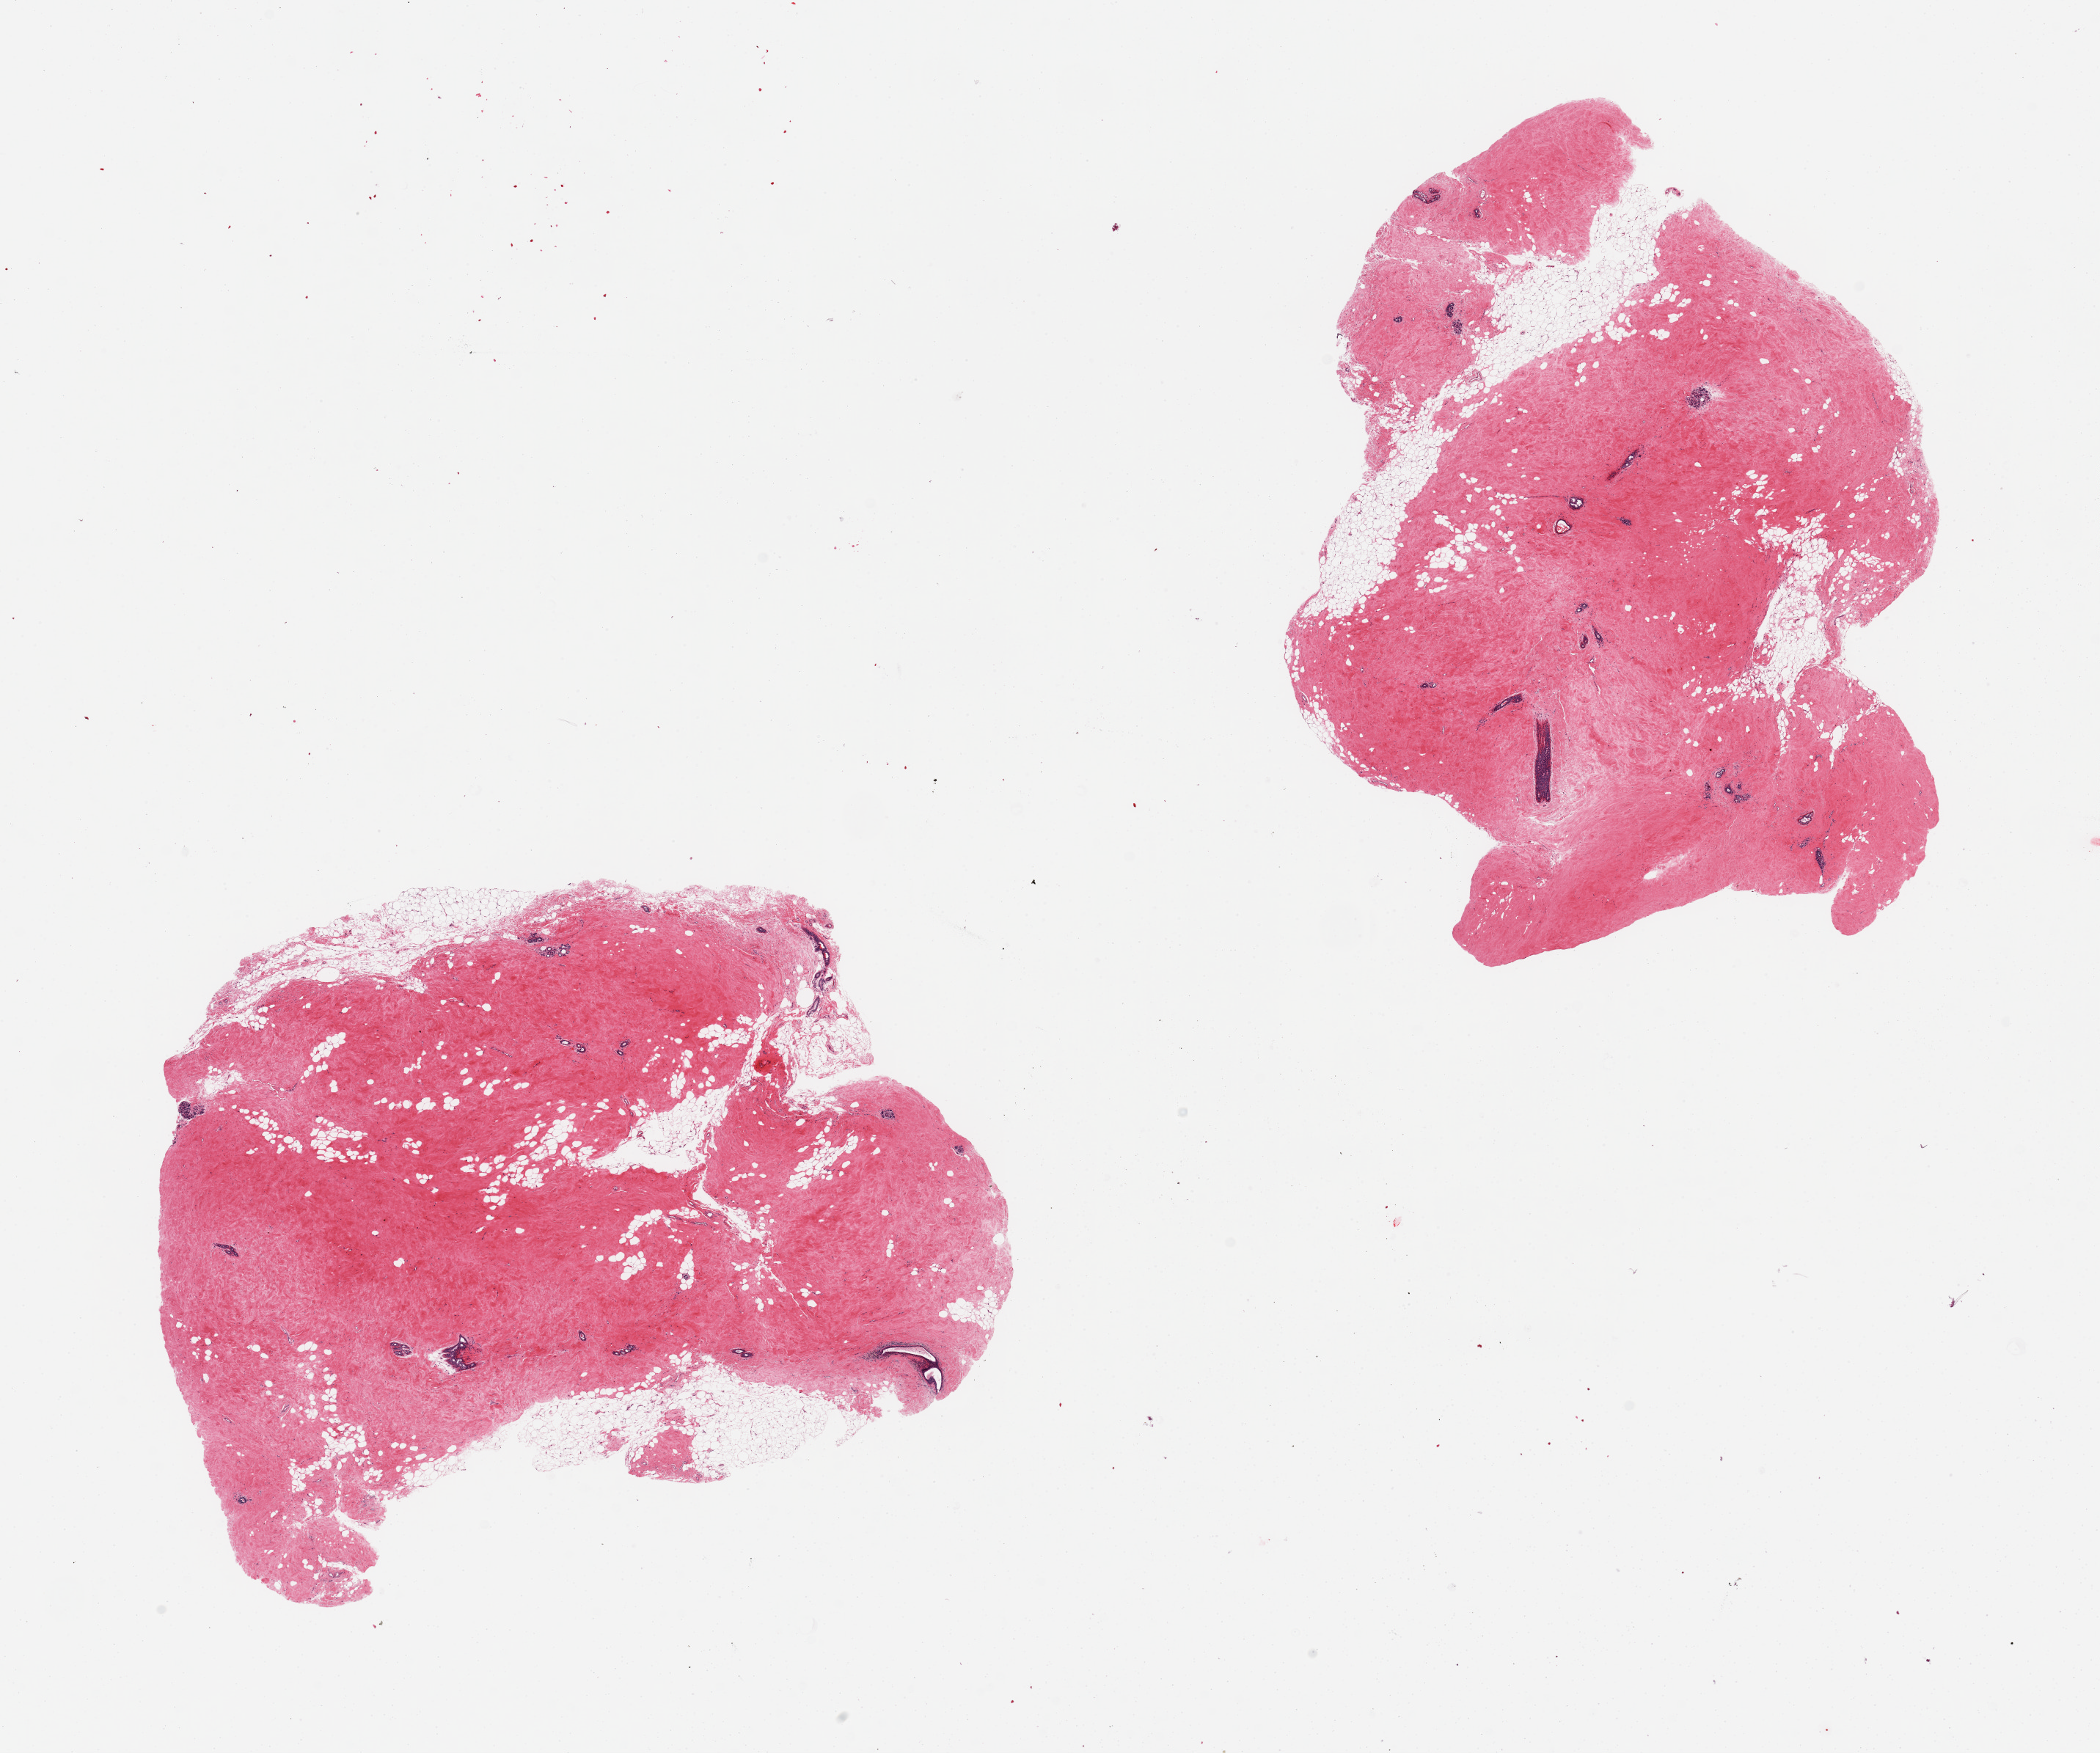
Hematoxylin and eosin (H&E) whole-slide image, brightfield — whole scanned area (about 22.6 x 18.9 mm, acquisition: 20x scan) shown as a low-resolution overview, PAXgene-fixed, paraffin-embedded tissue, target tissue: breast, donor tissue sample.
Review note (as recorded): 2 pieces, largely atrophic TDLUS, fibrous mastopathy.